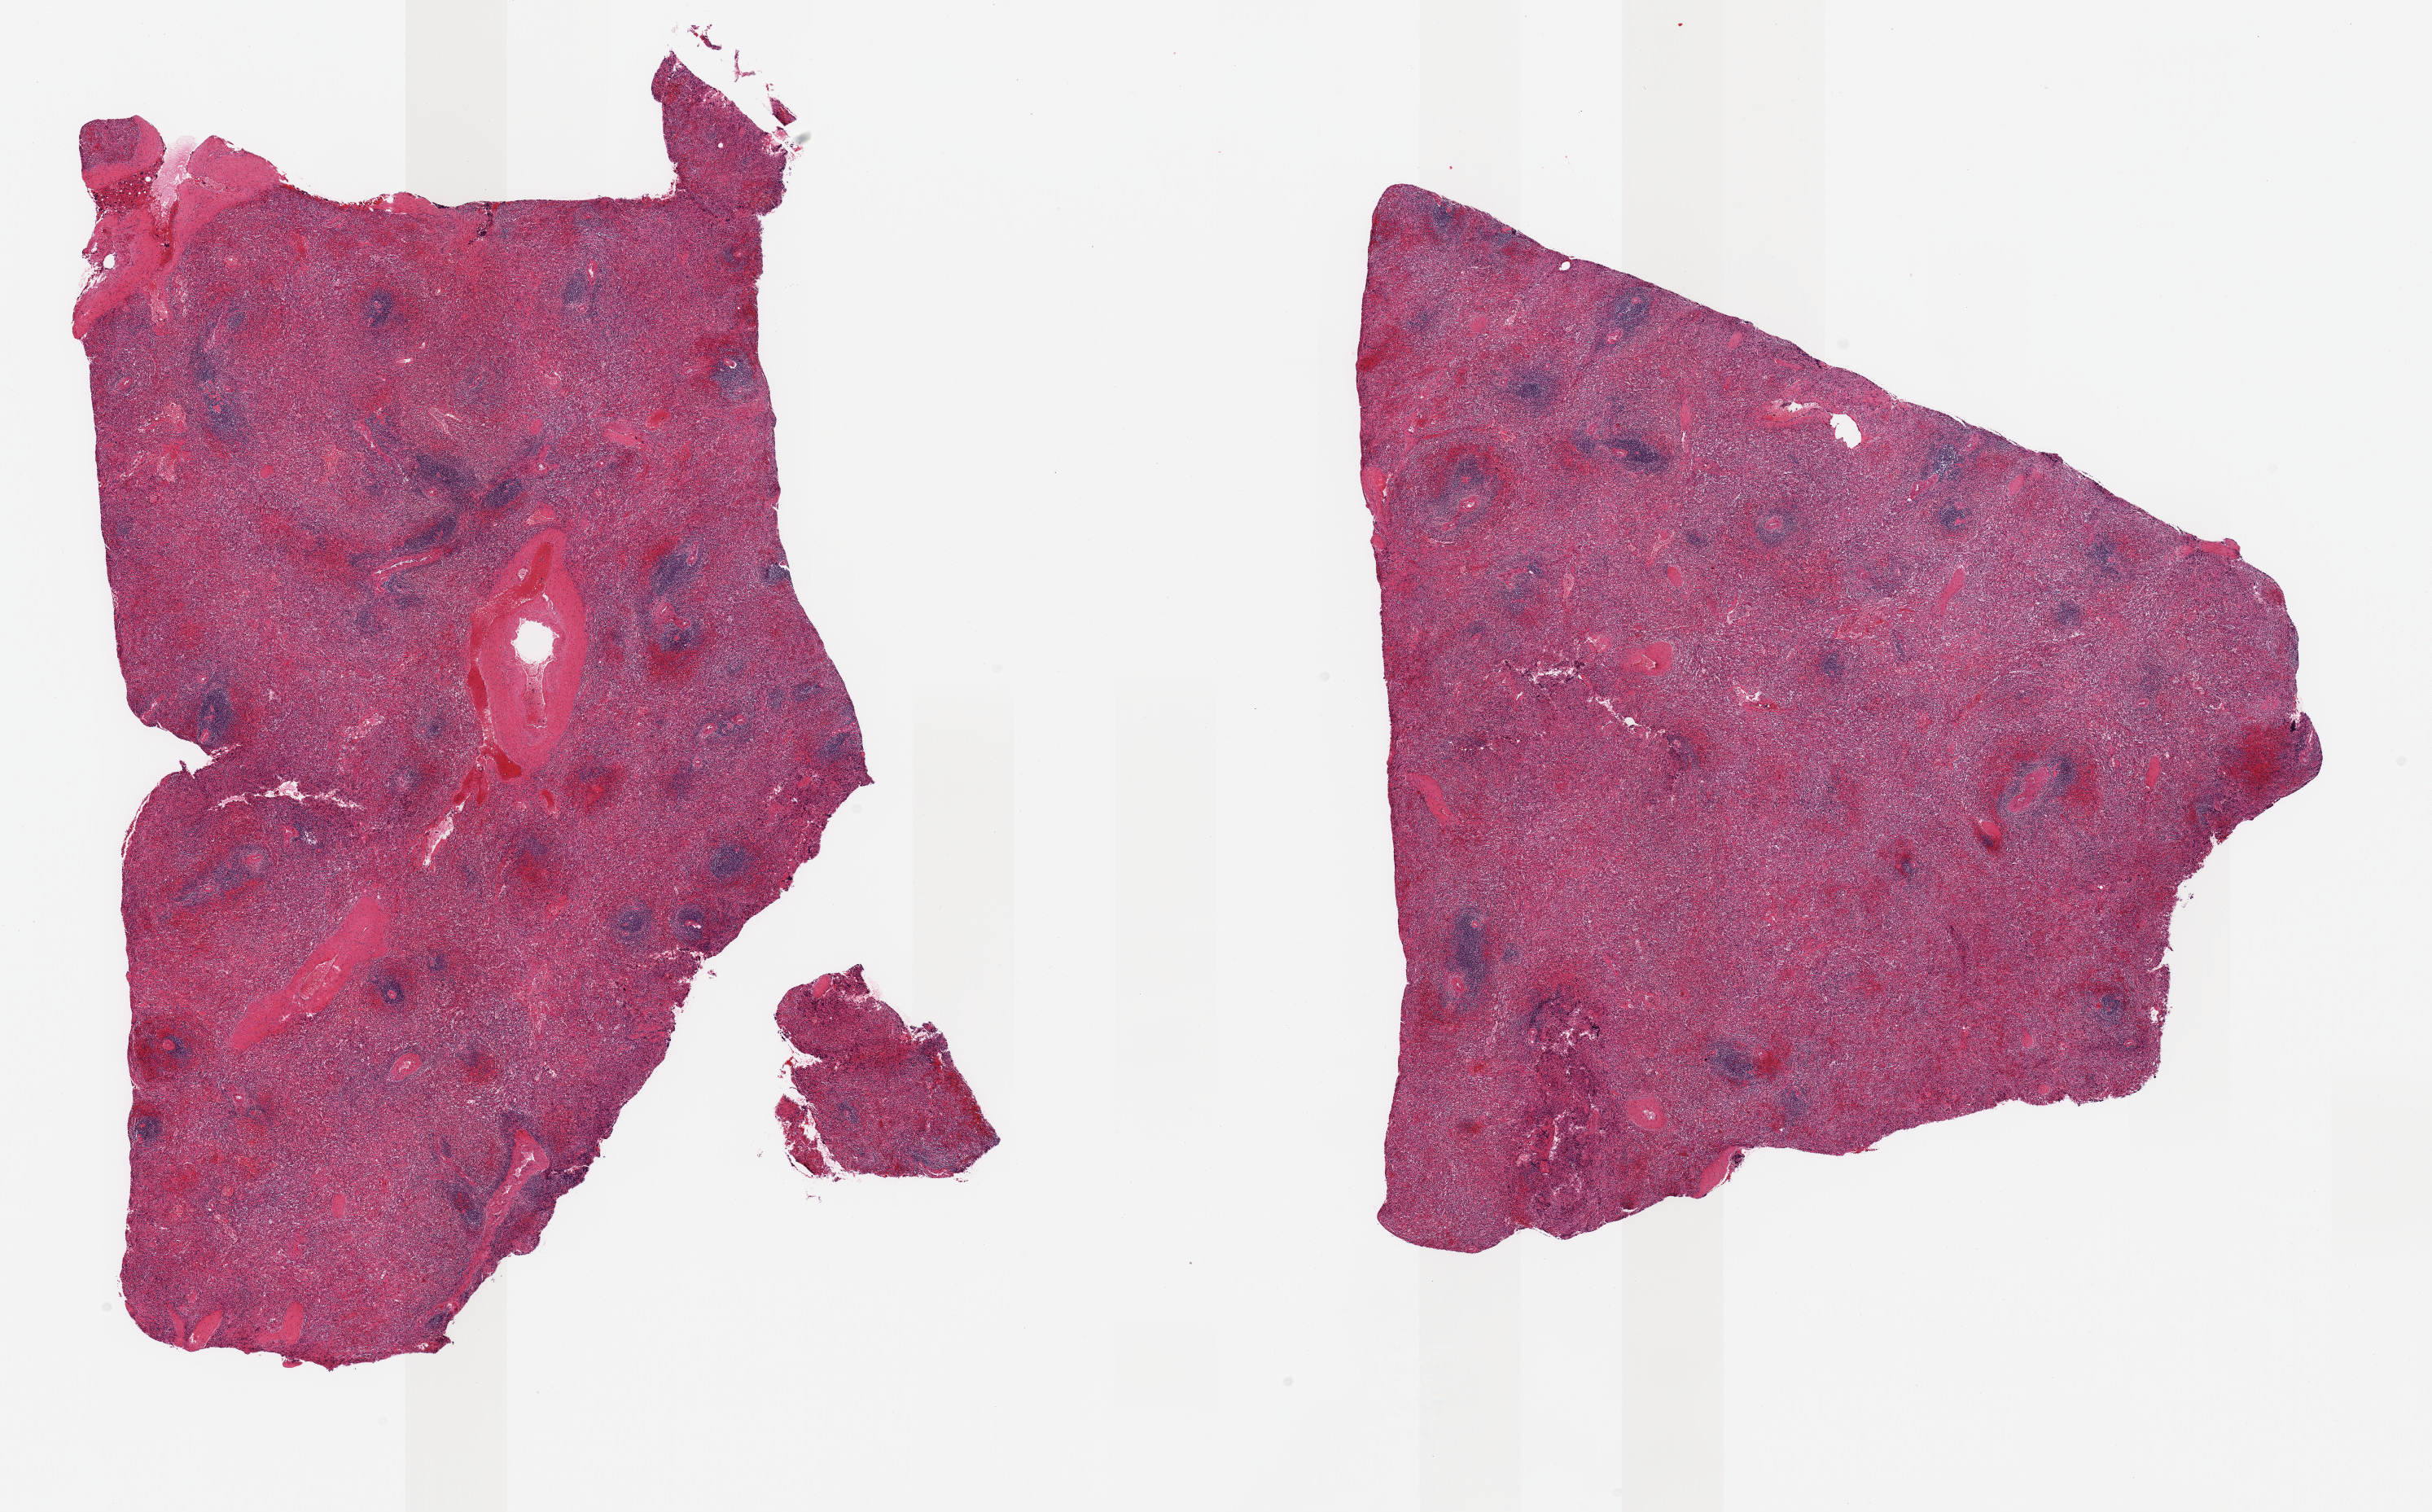
Haematoxylin and eosin whole-slide image, whole scanned area (about 23.6 x 14.7 mm) shown as a low-resolution overview, PAXgene-fixed paraffin-embedded (PFPE) section, sampled site (target tissue): spleen, donor tissue sample. Donor: male.
Pathologist's review note for this sample: 2 pieces, moderate congestion.